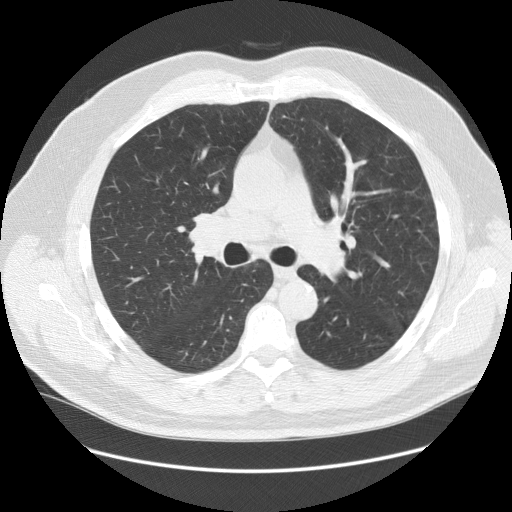
Axial slice from a low-dose chest CT screening exam; first (baseline) screen; lung window (W 1500 / L -600 HU); 2.5 mm slice thickness; 120 kVp; 512 × 512 image matrix. Male, age 64 years at enrolment. Former smoker at enrolment.
Lesion marked by an expert reader, bounding box (x1, y1, x2, y2) in pixels: (180, 199, 249, 269). Screening reader's record for this exam (one nodule recorded; not confirmed to be the boxed lesion): non-calcified nodule or mass ≥4 mm, right lower lobe, 7 × 5 mm, smooth margins, soft tissue attenuation. Official screen result: positive, change unspecified: nodule(s) >= 4 mm or enlarging nodule(s), mass(es), or other non-specific abnormalities suspicious for lung cancer.